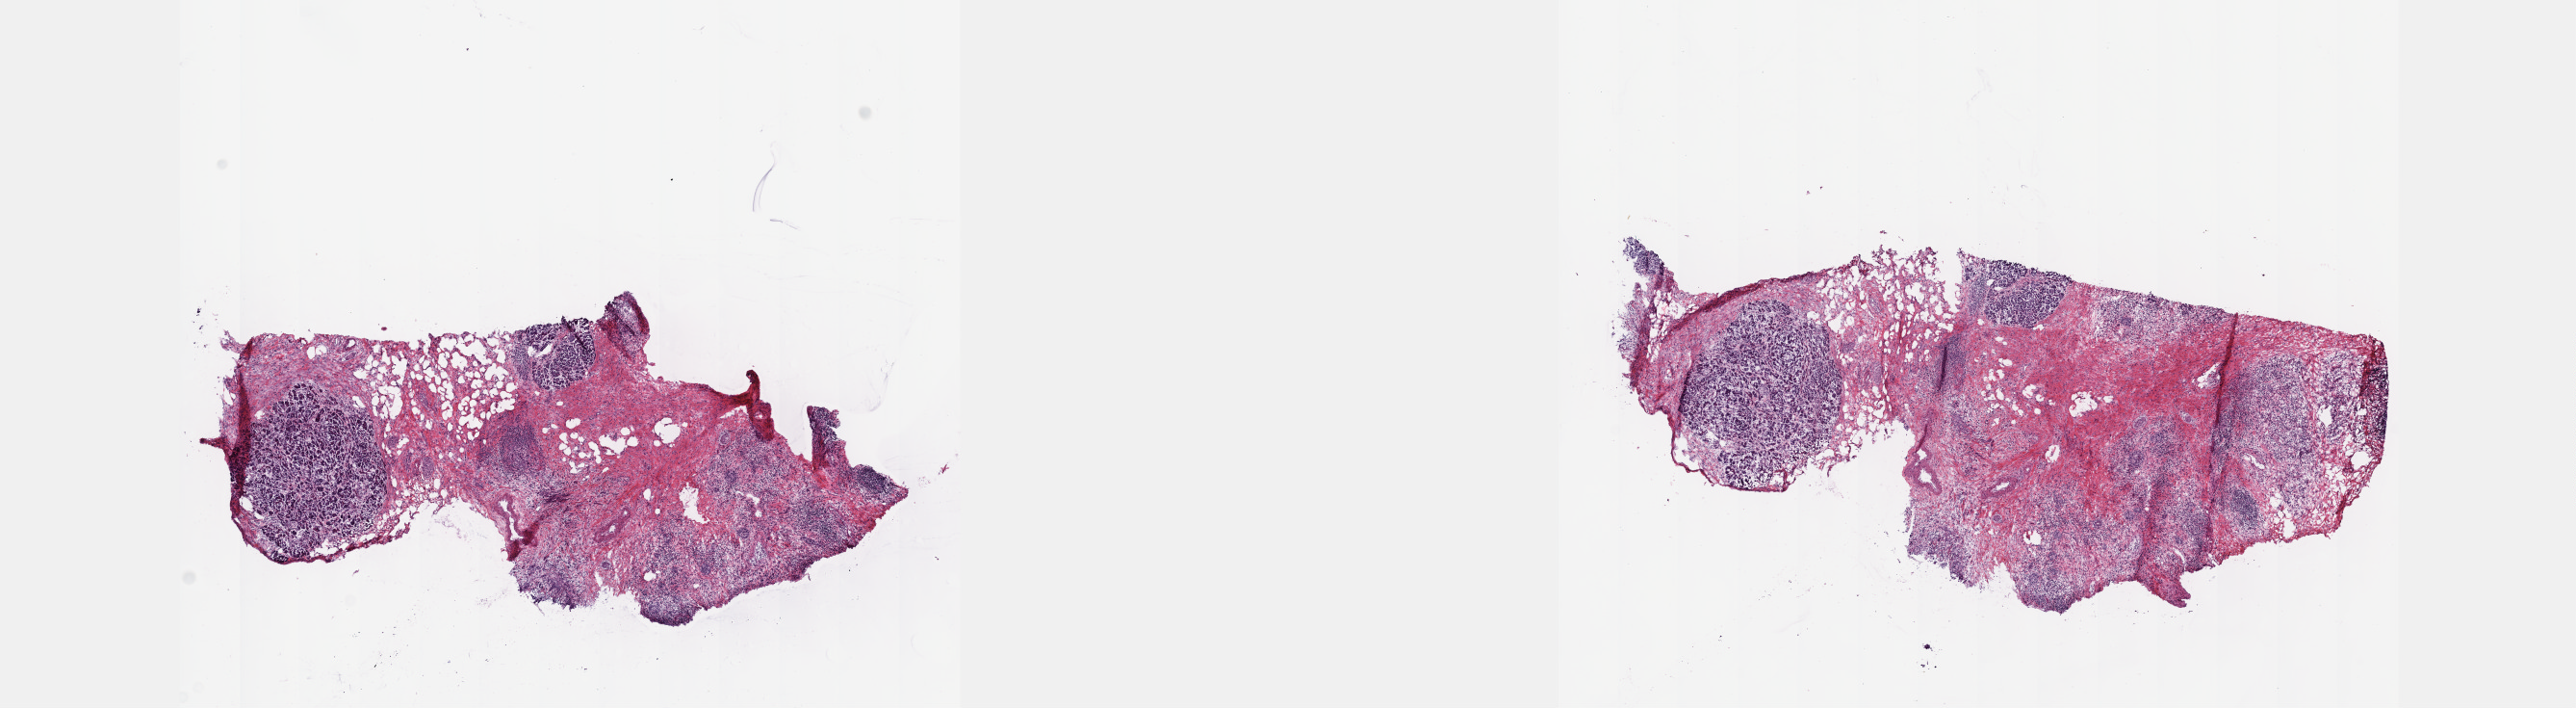
Digitized Hematoxylin and eosin (H&E) stained tissue section (whole slide), shown as a low-resolution overview of the whole scanned area (about 21.6 x 5.9 mm, from a 40x scan). Frozen section from the top of the tissue portion. Primary tumour sample from the pancreas. Male patient; age at initial diagnosis 77 years. Histologic grade: G3 (poorly differentiated). Slide review estimates, as recorded: tumour cells 50%, tumour nuclei 50%, normal cells 0%, stromal cells 40%, necrosis 10%. Inflammatory infiltration, as recorded: lymphocyte infiltration 40%, monocyte infiltration 20%, neutrophil infiltration 20%.
AJCC pathologic stage: IIB (7th edition). TNM: T3 N1 M0. Lymph nodes positive (case pathology): 7 of 19 examined. Histologic diagnosis: Infiltrating duct carcinoma, NOS (head of pancreas).